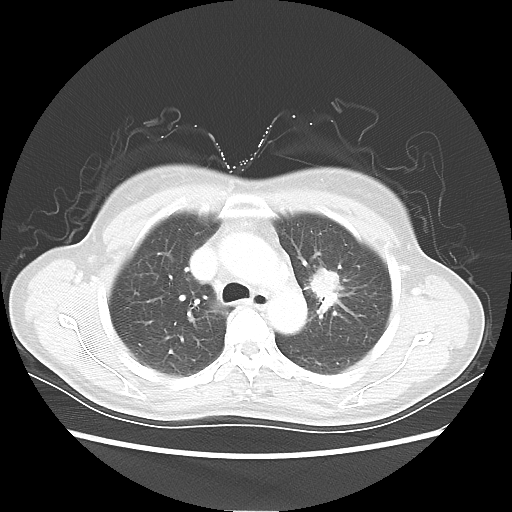
Chest CT, one axial slice. Slice 39 of 54 in the series (ordered by position). Lung window (W 1500 / L -600 HU). 512 × 512 image matrix, field of view 360 × 360 mm. Female patient, age 53 years. Case-level facts recorded for this patient, not image findings: clinical TNM (as recorded): T1c N0 M0.
Structures marked on this image (rectangle marked by the reading radiologist):
- lung tumour (recorded histology: adenocarcinoma): box from (x=301, y=259) to (x=346, y=309) px
- lung tumour (recorded histology: adenocarcinoma): (x=304, y=265)–(x=349, y=315)